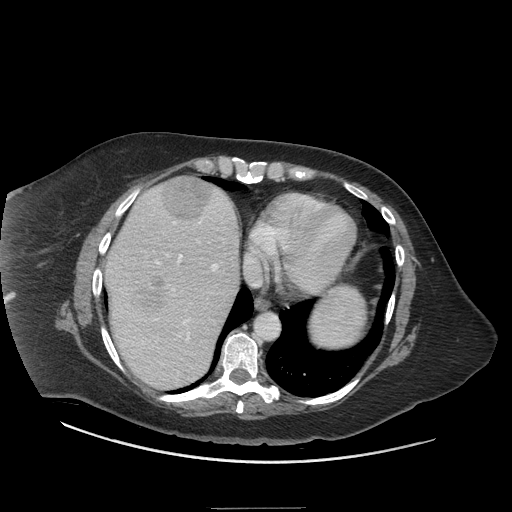
Contrast-enhanced abdominal CT (liver protocol), one axial slice; slice 59 of 81 in the series (ordered by position); reconstruction kernel STANDARD; 140 kVp; soft-tissue window (W 400 / L 40 HU); 2.5 mm slice thickness; 512 × 512 image matrix, field of view 440 × 440 mm. Case-level facts recorded for this patient, not image findings: diagnosis: hepatocellular carcinoma (patient treated with transarterial chemoembolisation; whether this scan precedes or follows treatment is not stated here); TNM stage (as recorded): Stage-II; Child-Pugh class: A; tumour differentiation: moderately differentiated; tumour nodularity: multinodular.
Structures marked on this image (semi-automatically segmented with operator editing):
- abdominal aorta: box from (x=254, y=313) to (x=279, y=340) px
- liver parenchyma outside the tumour (the mass and vessels are separate outlines, so this box may not span the whole liver): (x=104, y=178)–(x=238, y=388)
- mass: (x=136, y=177)–(x=213, y=314)
- liver vessels: (x=118, y=199)–(x=223, y=373)